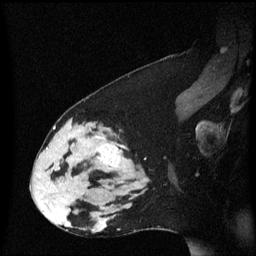
Breast MRI (dynamic contrast-enhanced), one sagittal slice. Slice 36 of 60 in the series (ordered by position). Dynamic contrast-enhanced series, image 2 of 3 at this slice position (ordered by acquisition). 1.5 T. TE 4.2 ms, TR 8.4 ms. 2 mm slice thickness. 256 × 256 image matrix. Female patient, age 33 years. From the clinical record (not read from this slice): setting: breast cancer imaged before/during neoadjuvant chemotherapy; receptor status: triple-negative.
Outlined on this slice (semi-automatic segmentation, software-assisted and operator-edited):
- analysis volume of interest (the breast-tissue region the enhancement analysis was run in; not a lesion): bounding box (x1, y1, x2, y2) in pixels: (44, 123, 139, 189)
- tumour enhancement mask (voxels above the 70 % enhancement threshold inside the analysis volume of interest): (57, 137, 122, 171)